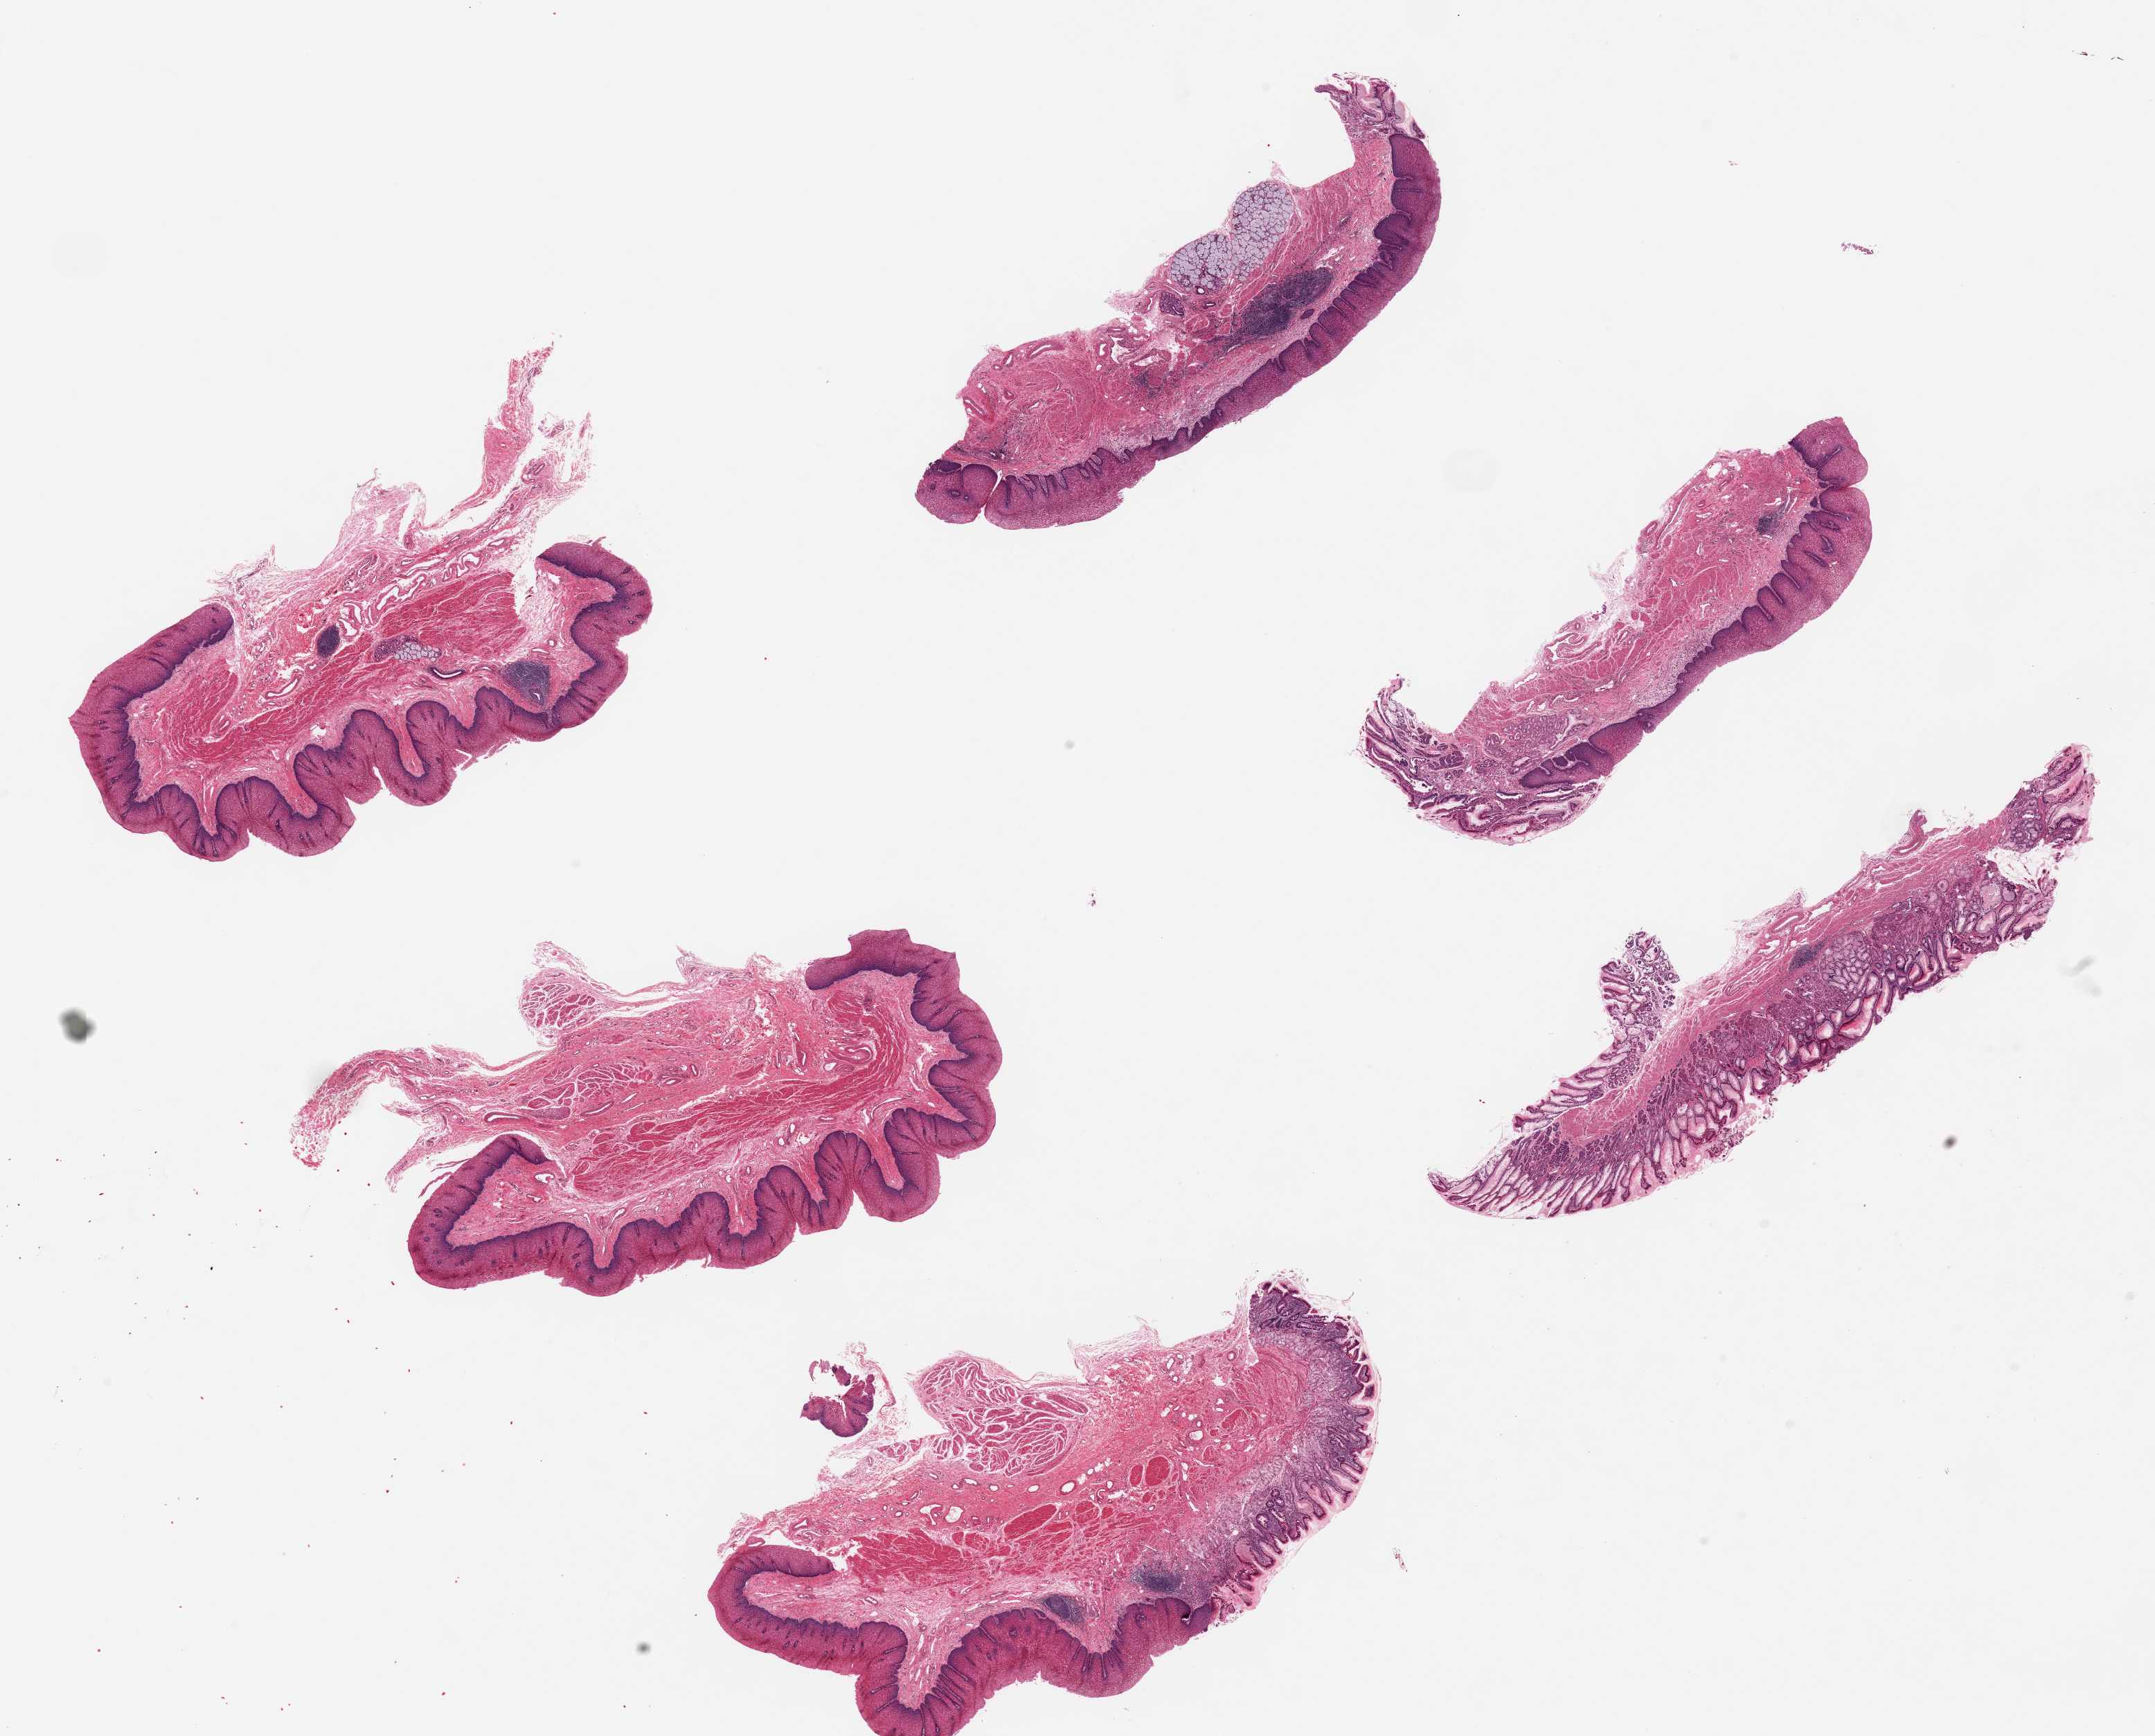
Hematoxylin and eosin (H&E) whole-slide image — low-resolution overview of the scanned area, about 24.6 x 19.8 mm; PAXgene-fixed paraffin-embedded (PFPE) section; section of esophageal mucous membrane (target tissue); donor tissue sample. Female donor.
Pathologist's review note for this sample: 6 pieces, ~6x2 mm, 3 have glandular mucosa in part or total; one shows intestinal metaplasia; several, squamous hyperplasia of reflux type.